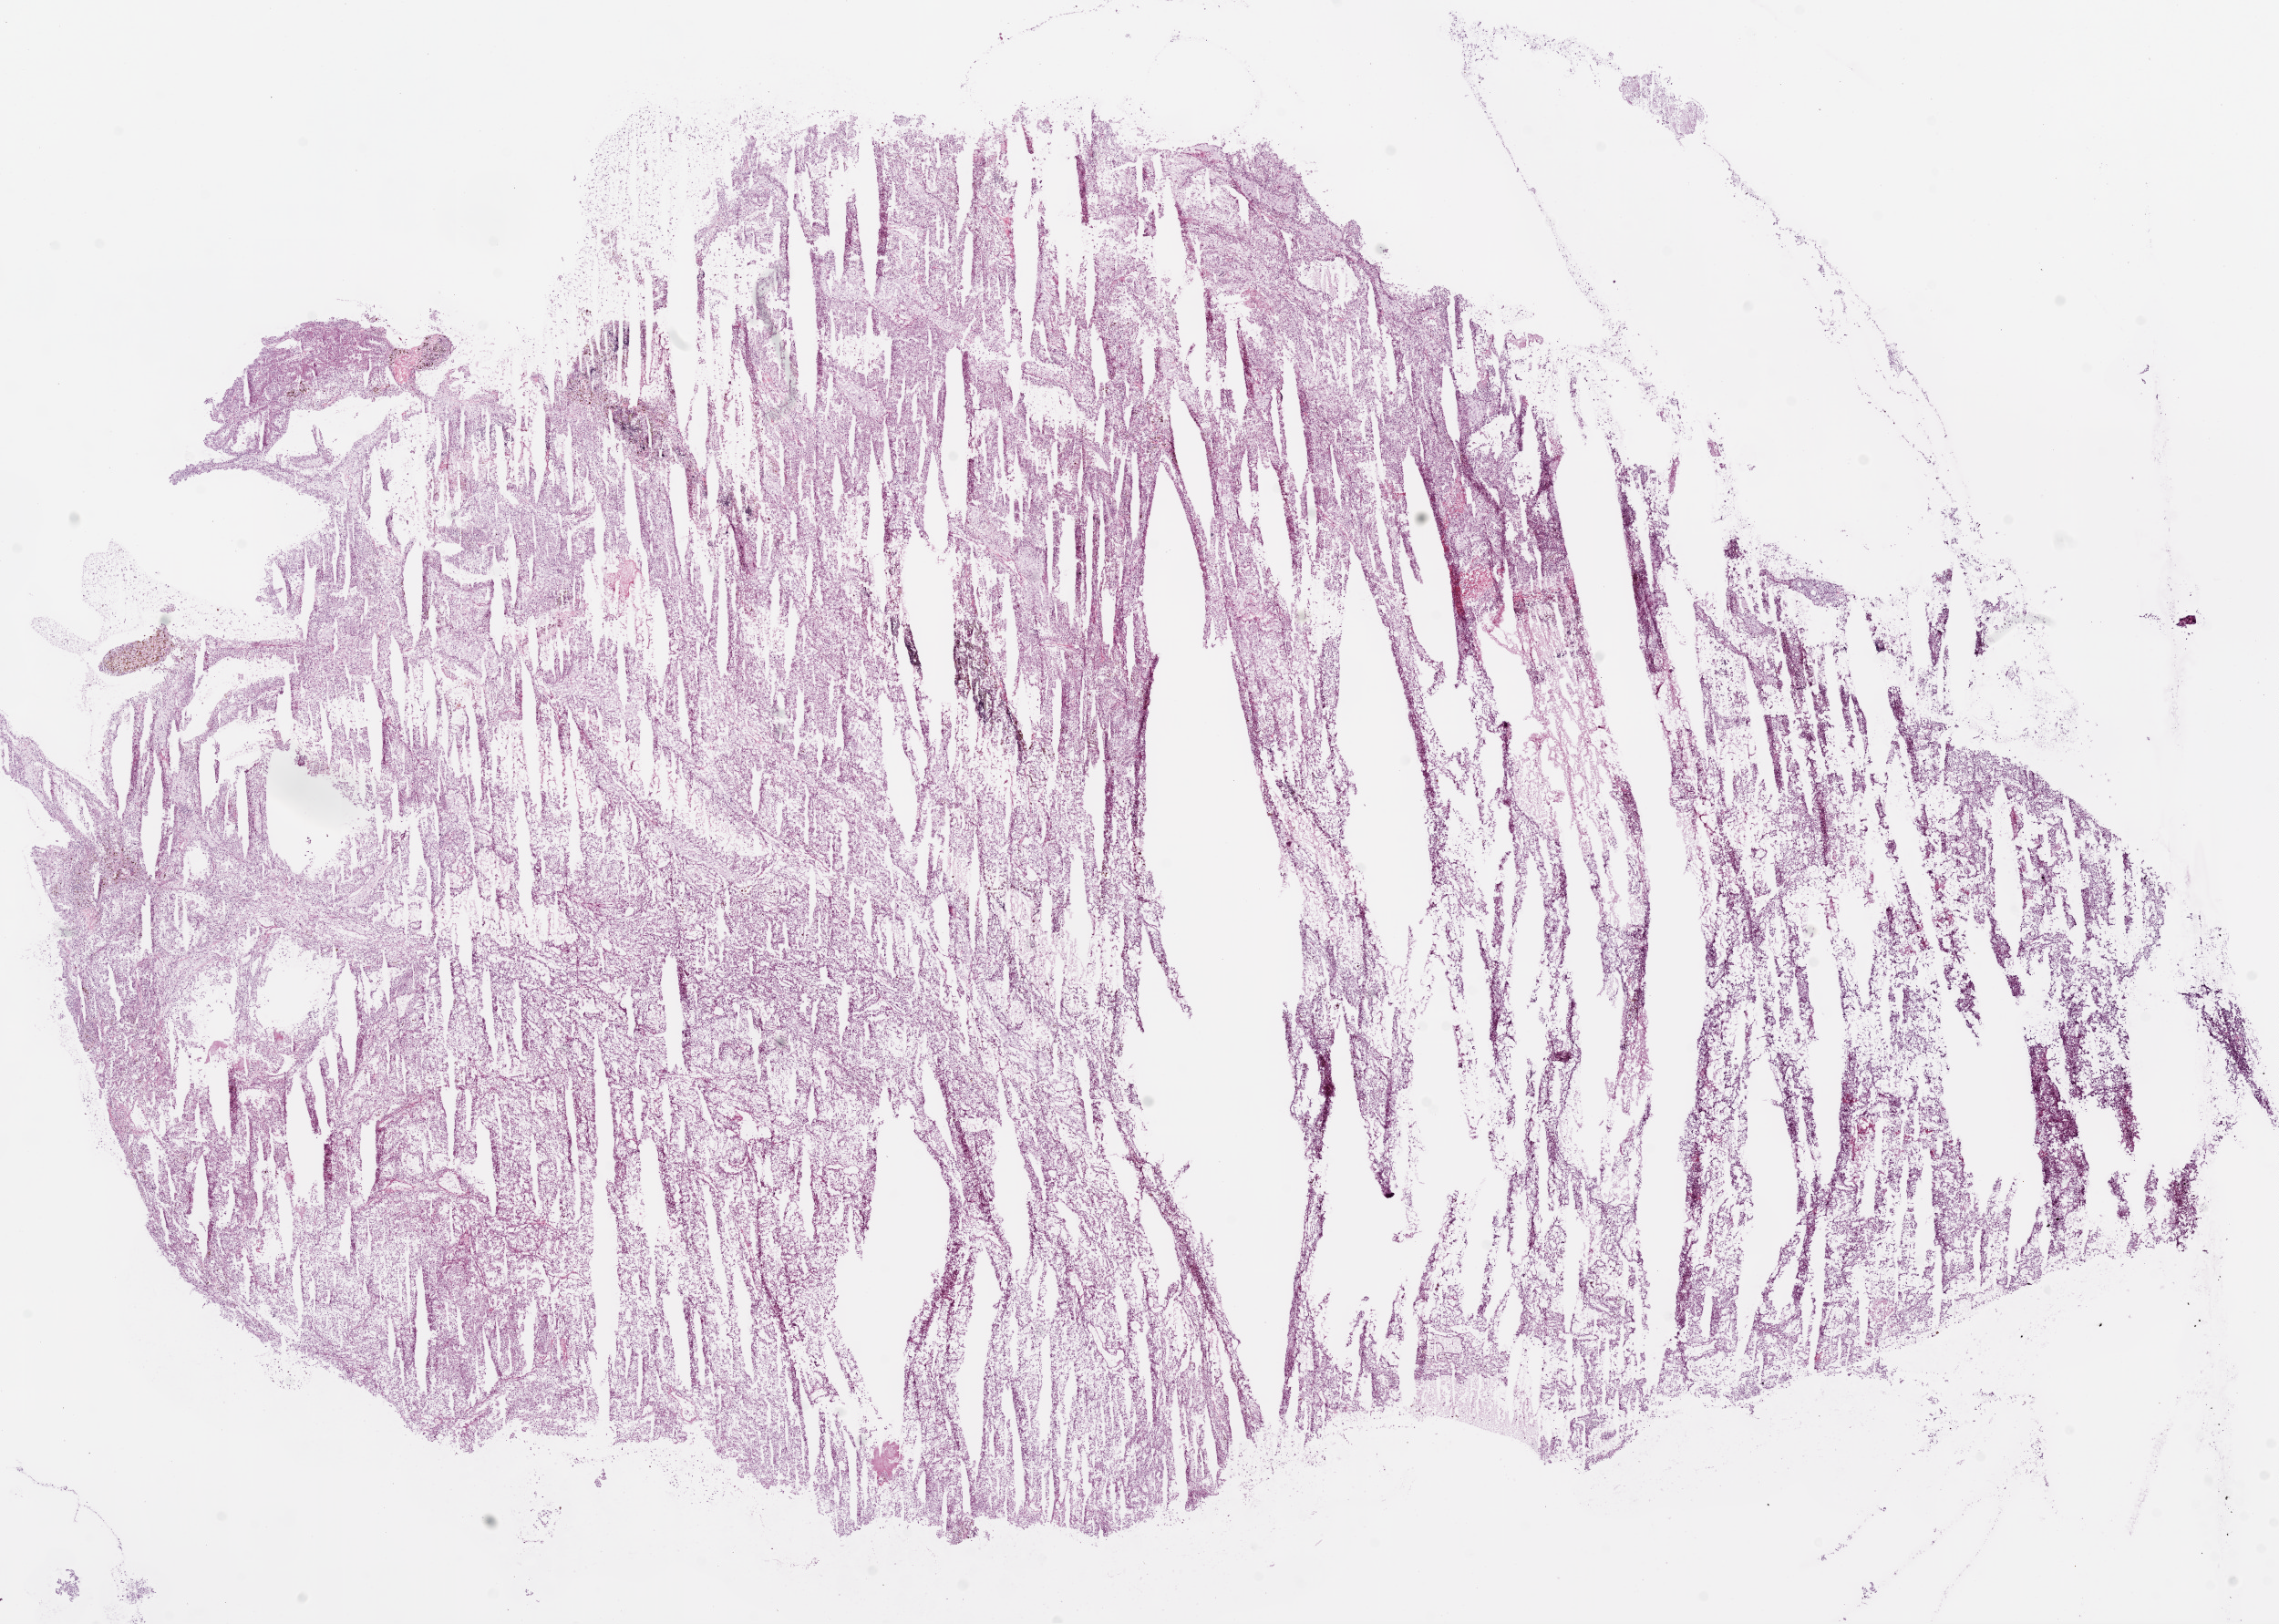
Hematoxylin and eosin (H&E) stained whole-slide image — shown as a low-resolution overview of the whole scanned area (about 20.1 x 14.3 mm). Frozen section from the top of the tissue portion. Kidney, primary tumour sample. Female patient; age at initial diagnosis 77 years. Histologic grade: G2 (moderately differentiated). Pathologist review of this section (percent, as recorded): tumour cells 85%, tumour nuclei 75%, normal cells 0%, stromal cells 10%, necrosis 5%.
- AJCC pathologic stage: III
- histologic diagnosis: Clear cell adenocarcinoma, NOS